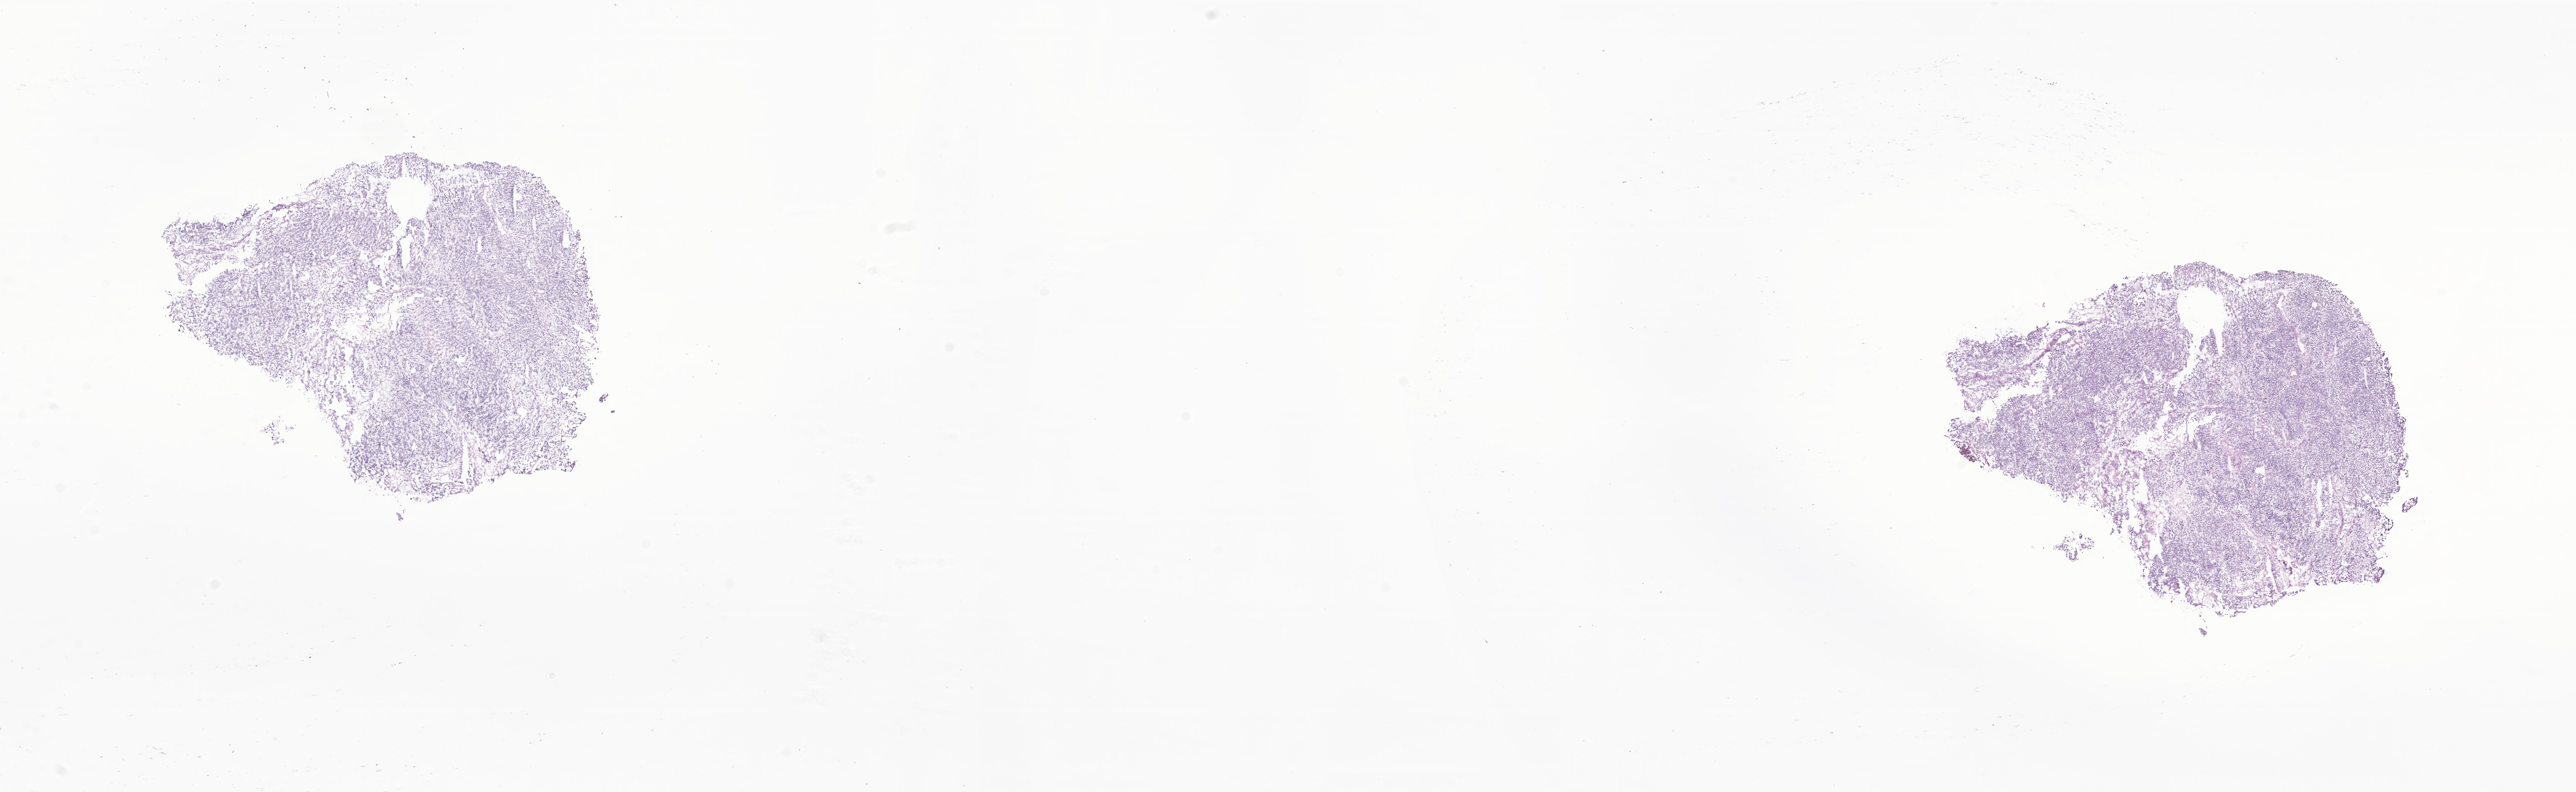
Digitized haematoxylin and eosin-stained section of tumor tissue from the adrenal gland, low-resolution overview of the scanned area, about 28.7 x 8.8 mm, frozen section (OCT-embedded). Patient: male, age 312 days.
- recorded diagnosis: Neuroblastoma, NOS